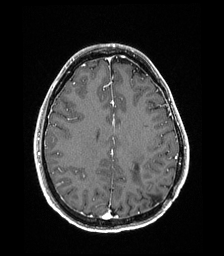
Brain MRI from a brain-tumour surgery series, one axial slice; slice 72 of 192 in the series (ordered by position); T1-weighted post-contrast; 1 mm slice thickness; 224 × 256 image matrix, field of view 224 × 256 mm. Case-level facts recorded for this patient, not image findings: histopathology: Low grade glioma; IDH mutation: no; tumour location: Left Parieto-Occipital Intraventricular.
Outlined on this slice (outlined manually by an expert reader):
- previous resection cavity: box from (x=153, y=199) to (x=159, y=203) px